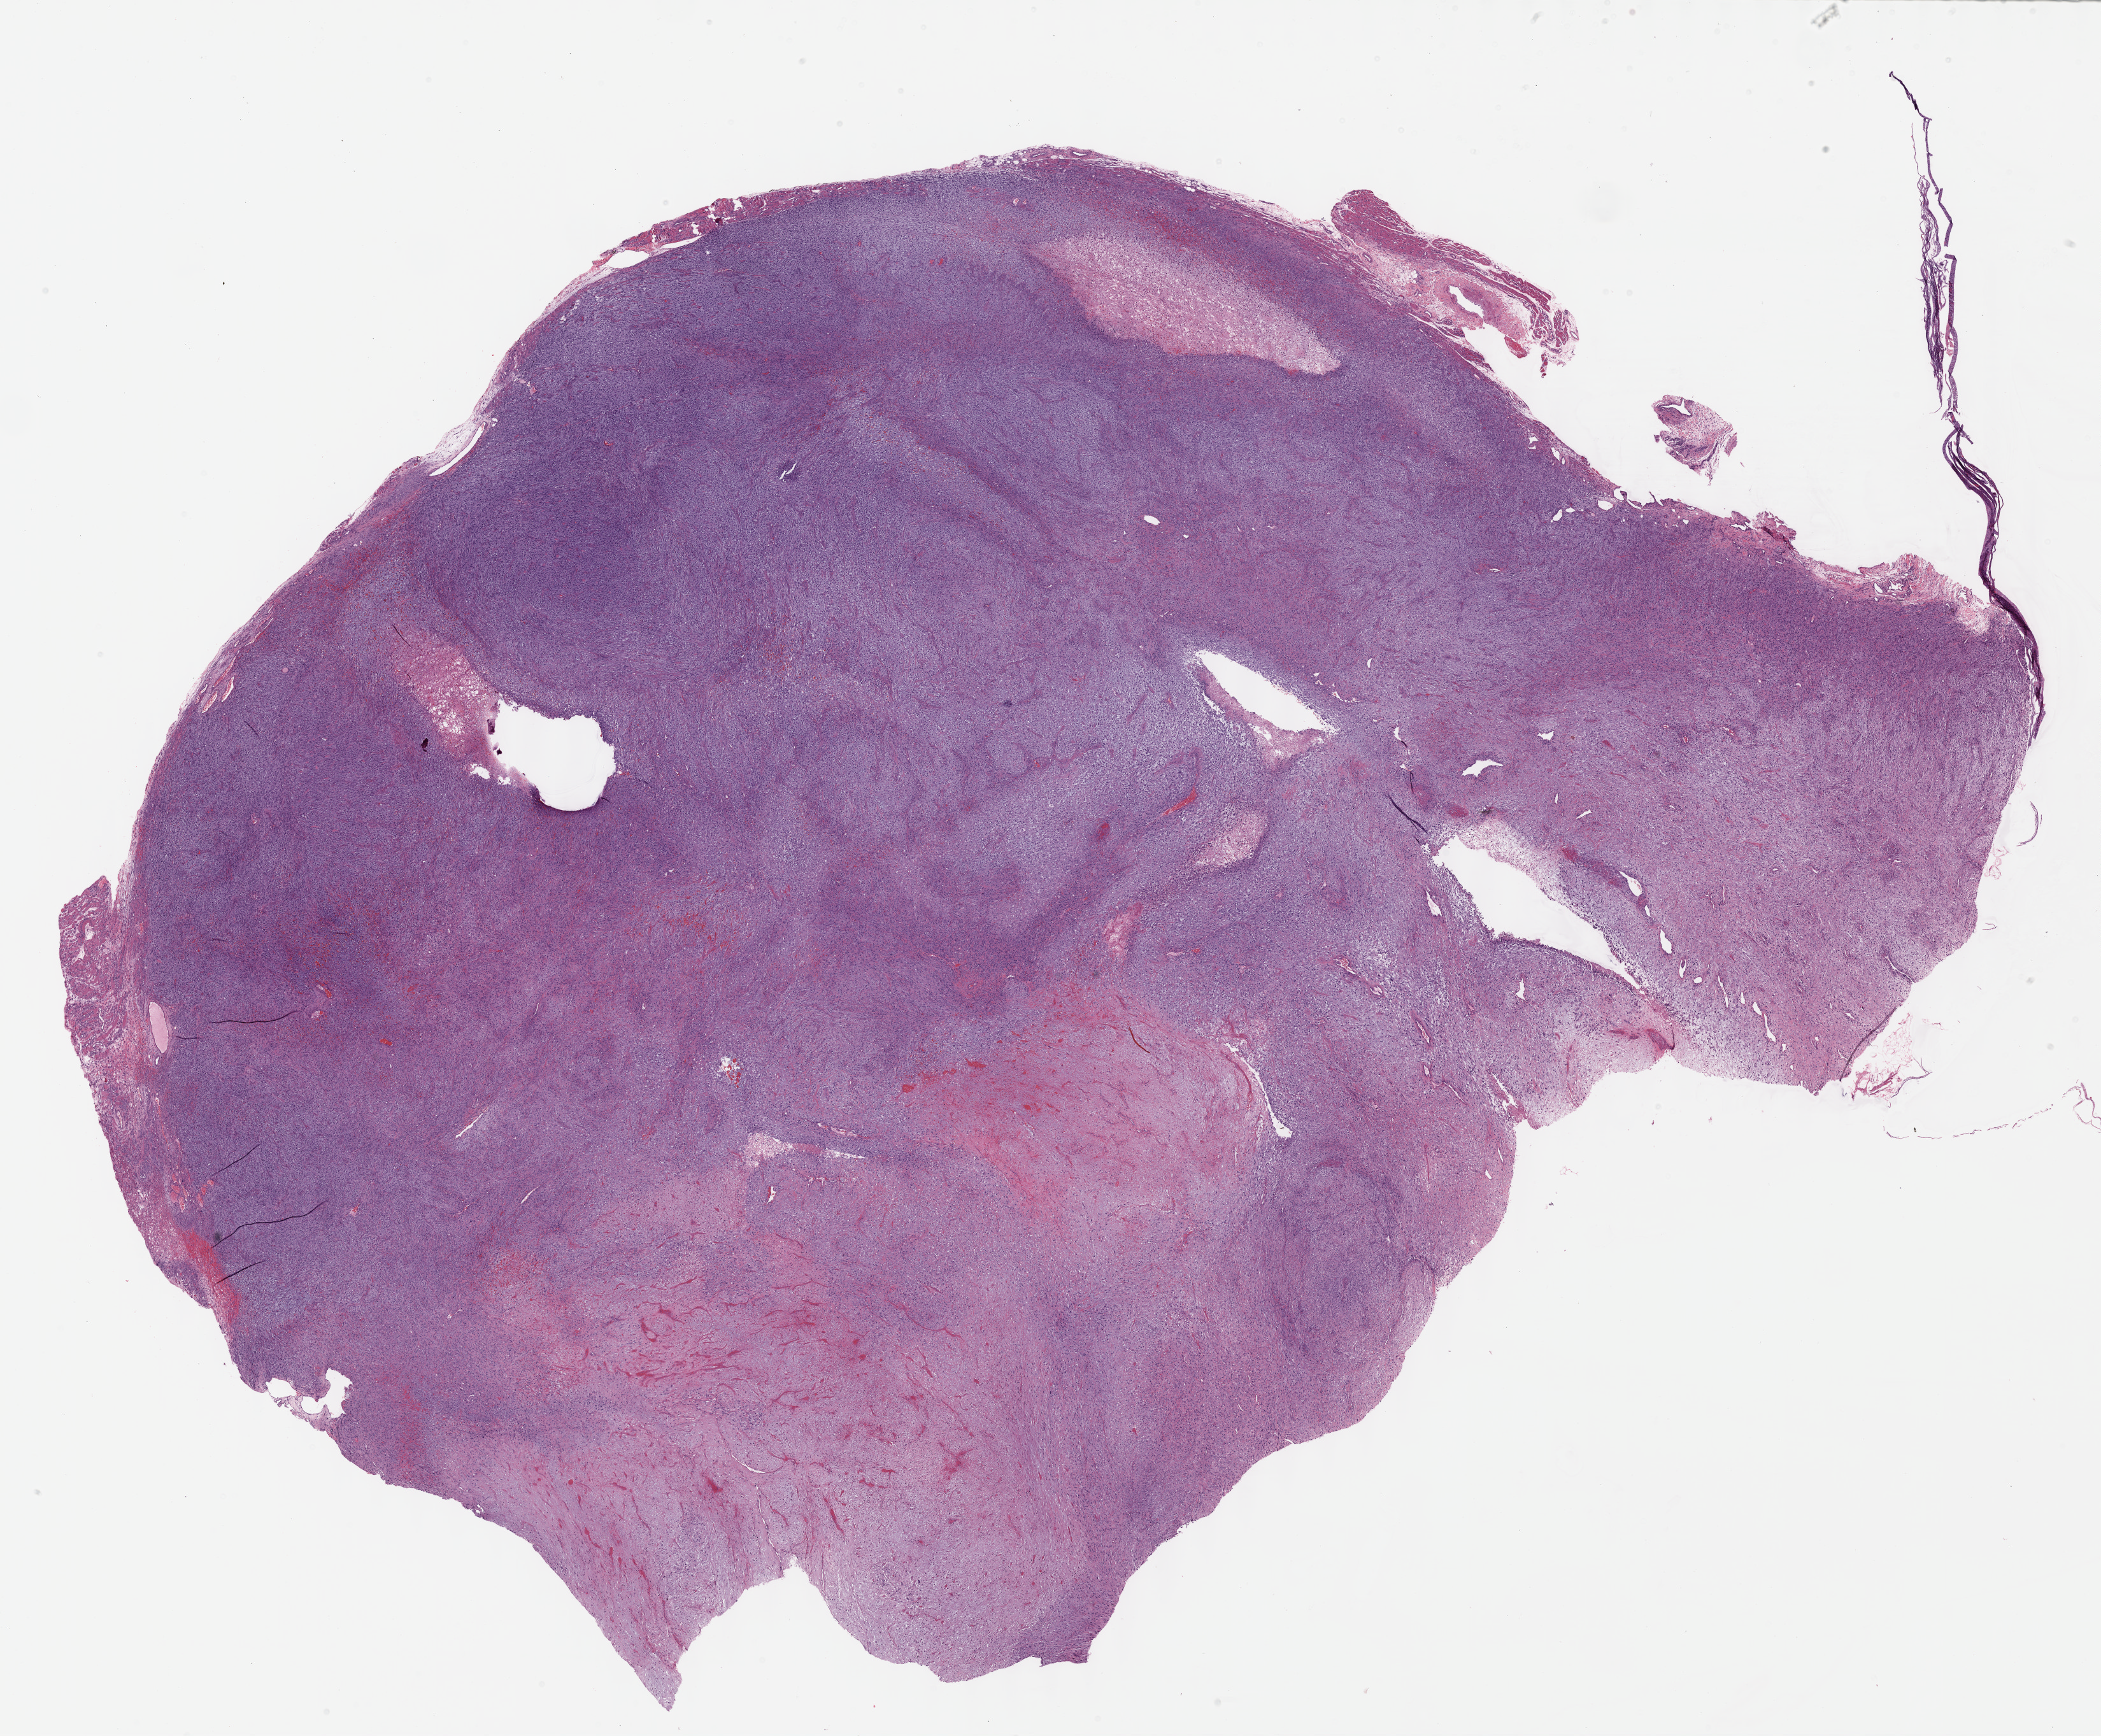
Whole-slide histology image, Hematoxylin and eosin (H&E) stained — shown as a low-resolution overview of the whole scanned area (about 26.7 x 22.0 mm, acquisition: 40x scan). Formalin-fixed paraffin-embedded (FFPE) diagnostic section. Connective, subcutaneous and other soft tissues, primary tumour sample. Female patient.
Diagnosis: Undifferentiated sarcoma.